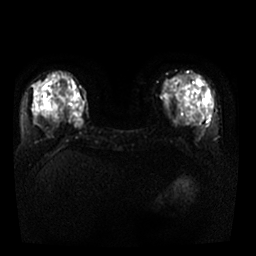
Breast MRI, one axial slice; position 13 of 29 along the scan axis; diffusion-weighted series; image 2 of 4 stored at this slice position (different b-values; order by instance number); 1.5 T; 256 × 256 image matrix, field of view 340 × 340 mm. Female patient.
Outlined on this slice (manually delineated by an expert):
- tumour on diffusion-weighted imaging: bounding box <74,119,83,129> (left, top, right, bottom; pixels)